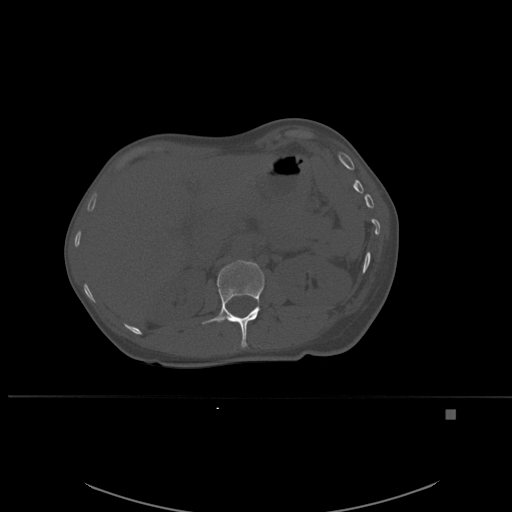
CT including the spine, one axial slice. Position 258 of 537 along the scan axis. Bone window (W 1800 / L 400 HU). 512 × 512 image matrix, field of view 440 × 440 mm. Patient: female, 45 years. Case-level facts recorded for this patient, not image findings: primary cancer: lung.
Annotated regions visible in this slice (semi-automatic segmentation, software-assisted and operator-edited):
- L1 vertebra: bounding box (x1, y1, x2, y2) in pixels: (202, 260, 265, 348)